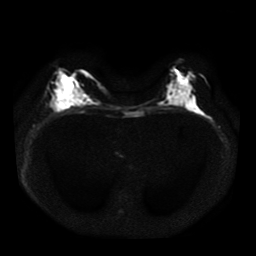
Breast MRI, one axial slice. Position 19 of 41 along the scan axis. Diffusion-weighted series; image 2 of 4 stored at this slice position (different b-values; order by instance number). 1.5 T. 5 mm slice thickness. 256 × 256 image matrix, field of view 330 × 330 mm. Female patient.
Structures marked on this image (expert manual segmentation):
- tumour on diffusion-weighted imaging: bounding box [x1, y1, x2, y2] px = [55, 103, 63, 109]